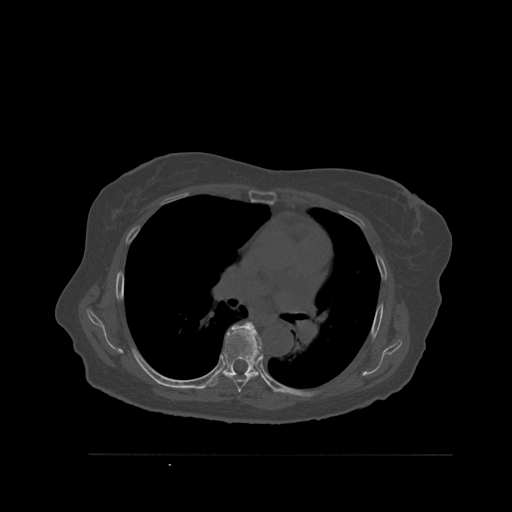
CT including the spine, one axial slice; position 373 of 527 along the scan axis; bone window (W 1800 / L 400 HU); 1.5 mm slice thickness; 512 × 512 image matrix, field of view 470 × 470 mm. Patient: female, 73 years. Case-level facts recorded for this patient, not image findings: primary cancer: breast.
Outlined on this slice (semi-automatically segmented with operator editing):
- T6 vertebra: box from (x=226, y=355) to (x=261, y=393) px
- T7 vertebra: (x=207, y=322)–(x=263, y=387)